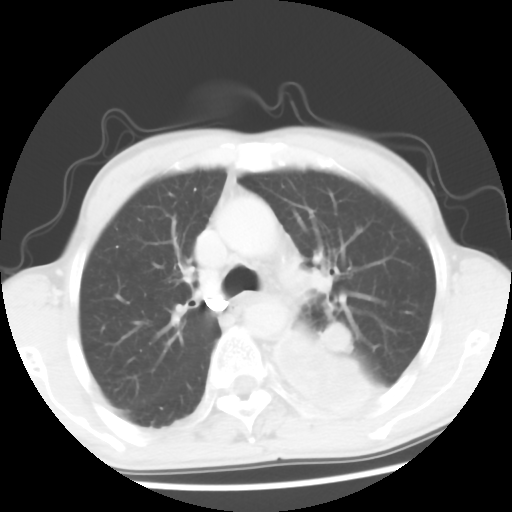
Chest CT, one axial slice; slice 39 of 56 in the series (ordered by position); 120 kVp; lung window (W 1500 / L -600 HU); 512 × 512 image matrix, field of view 318 × 318 mm. Male patient, age 60 years. From the clinical record (not read from this slice): clinical TNM (as recorded): T4 N0 M0.
Outlined on this slice (bounding box drawn by a radiologist):
- lung tumour (recorded histology: squamous cell carcinoma): box from (x=261, y=320) to (x=395, y=419) px